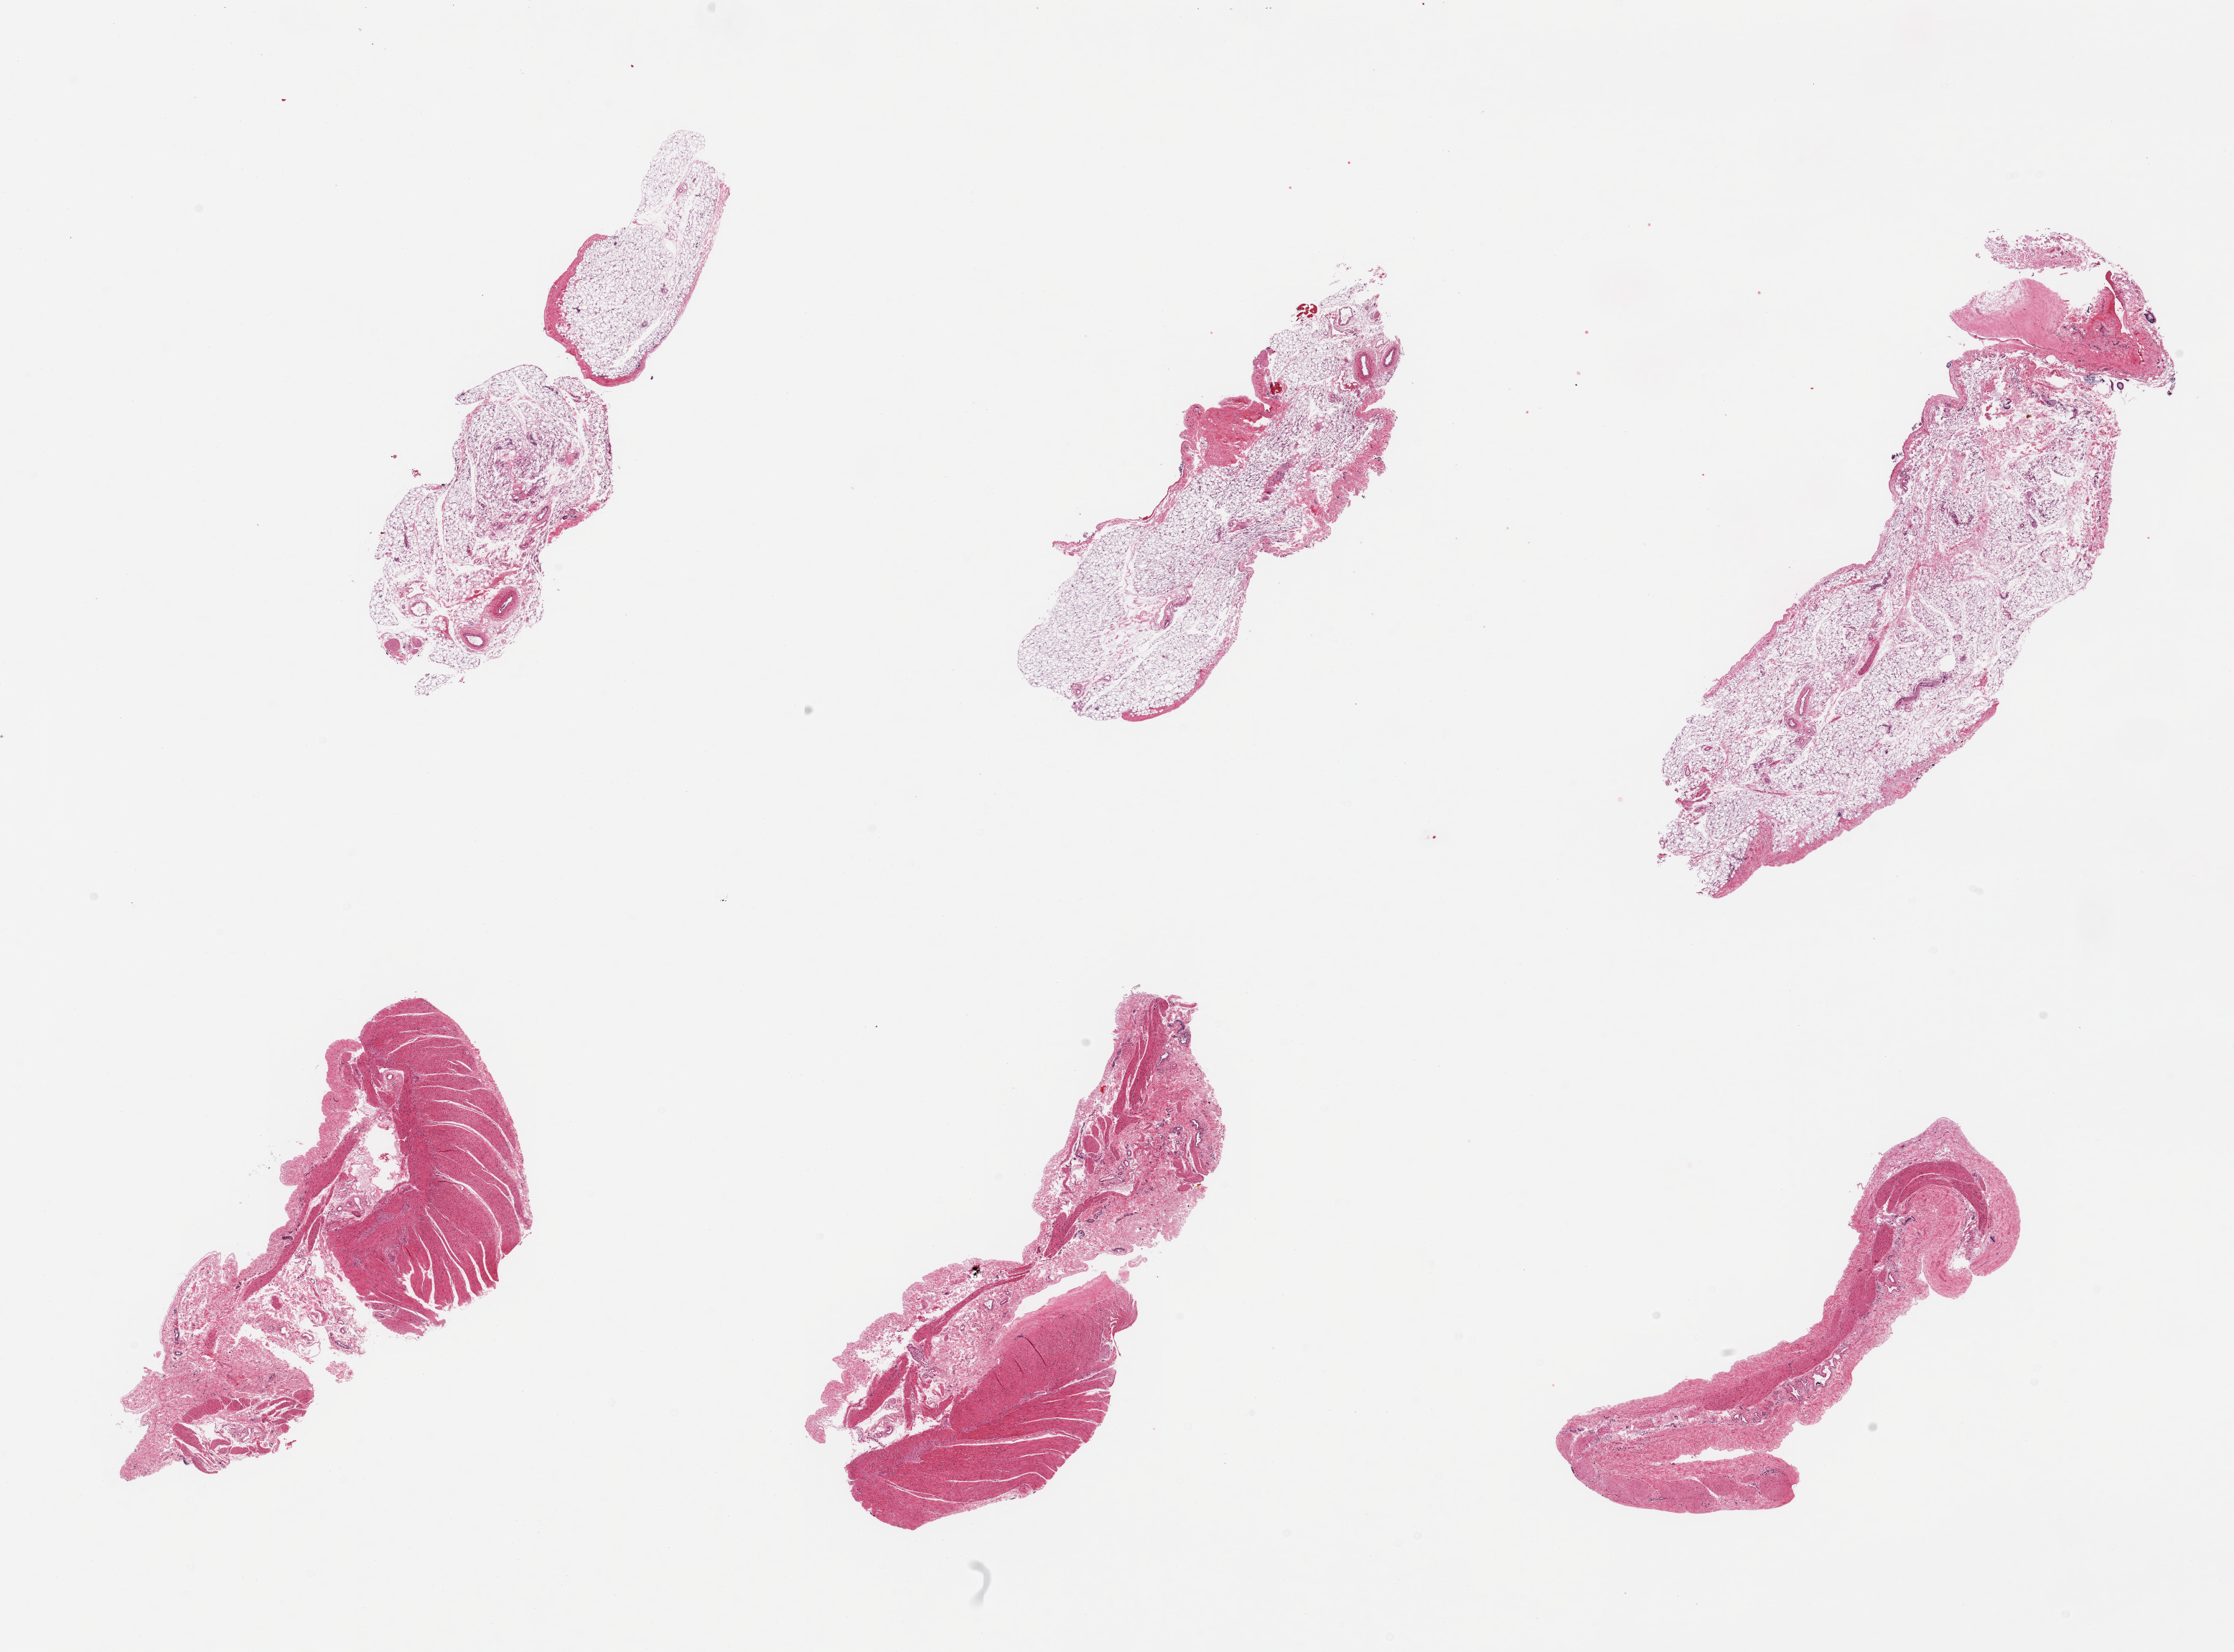
Digitized haematoxylin and eosin-stained section, low-resolution overview of the scanned area, about 24.6 x 18.2 mm, PAXgene-fixed, paraffin-embedded tissue, target tissue: ileum, tissue donor sample. Male donor.
Review note (as recorded): 6 pieces; all have muscularis and fat, no mucosa or lymphoid tissue.